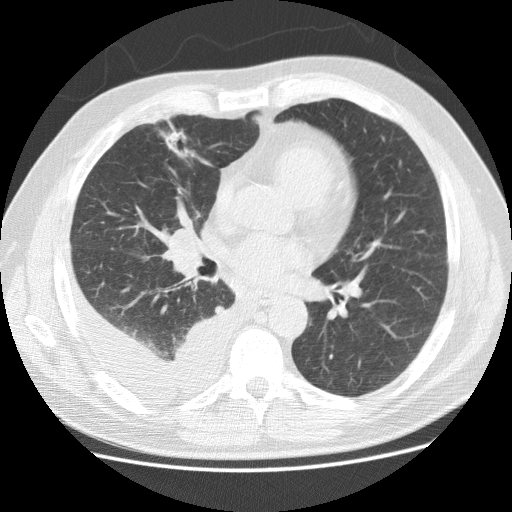
Low-dose screening chest CT, one axial slice. Position 63 of 142 along the scan axis. Lung window (W 1500 / L -600 HU). 512 × 512 image matrix.
Outlined on this slice (manually delineated by an expert):
- lesion 1 (tumor, middle lobe of right lung): bounding box <165,128,191,159> (left, top, right, bottom; pixels)